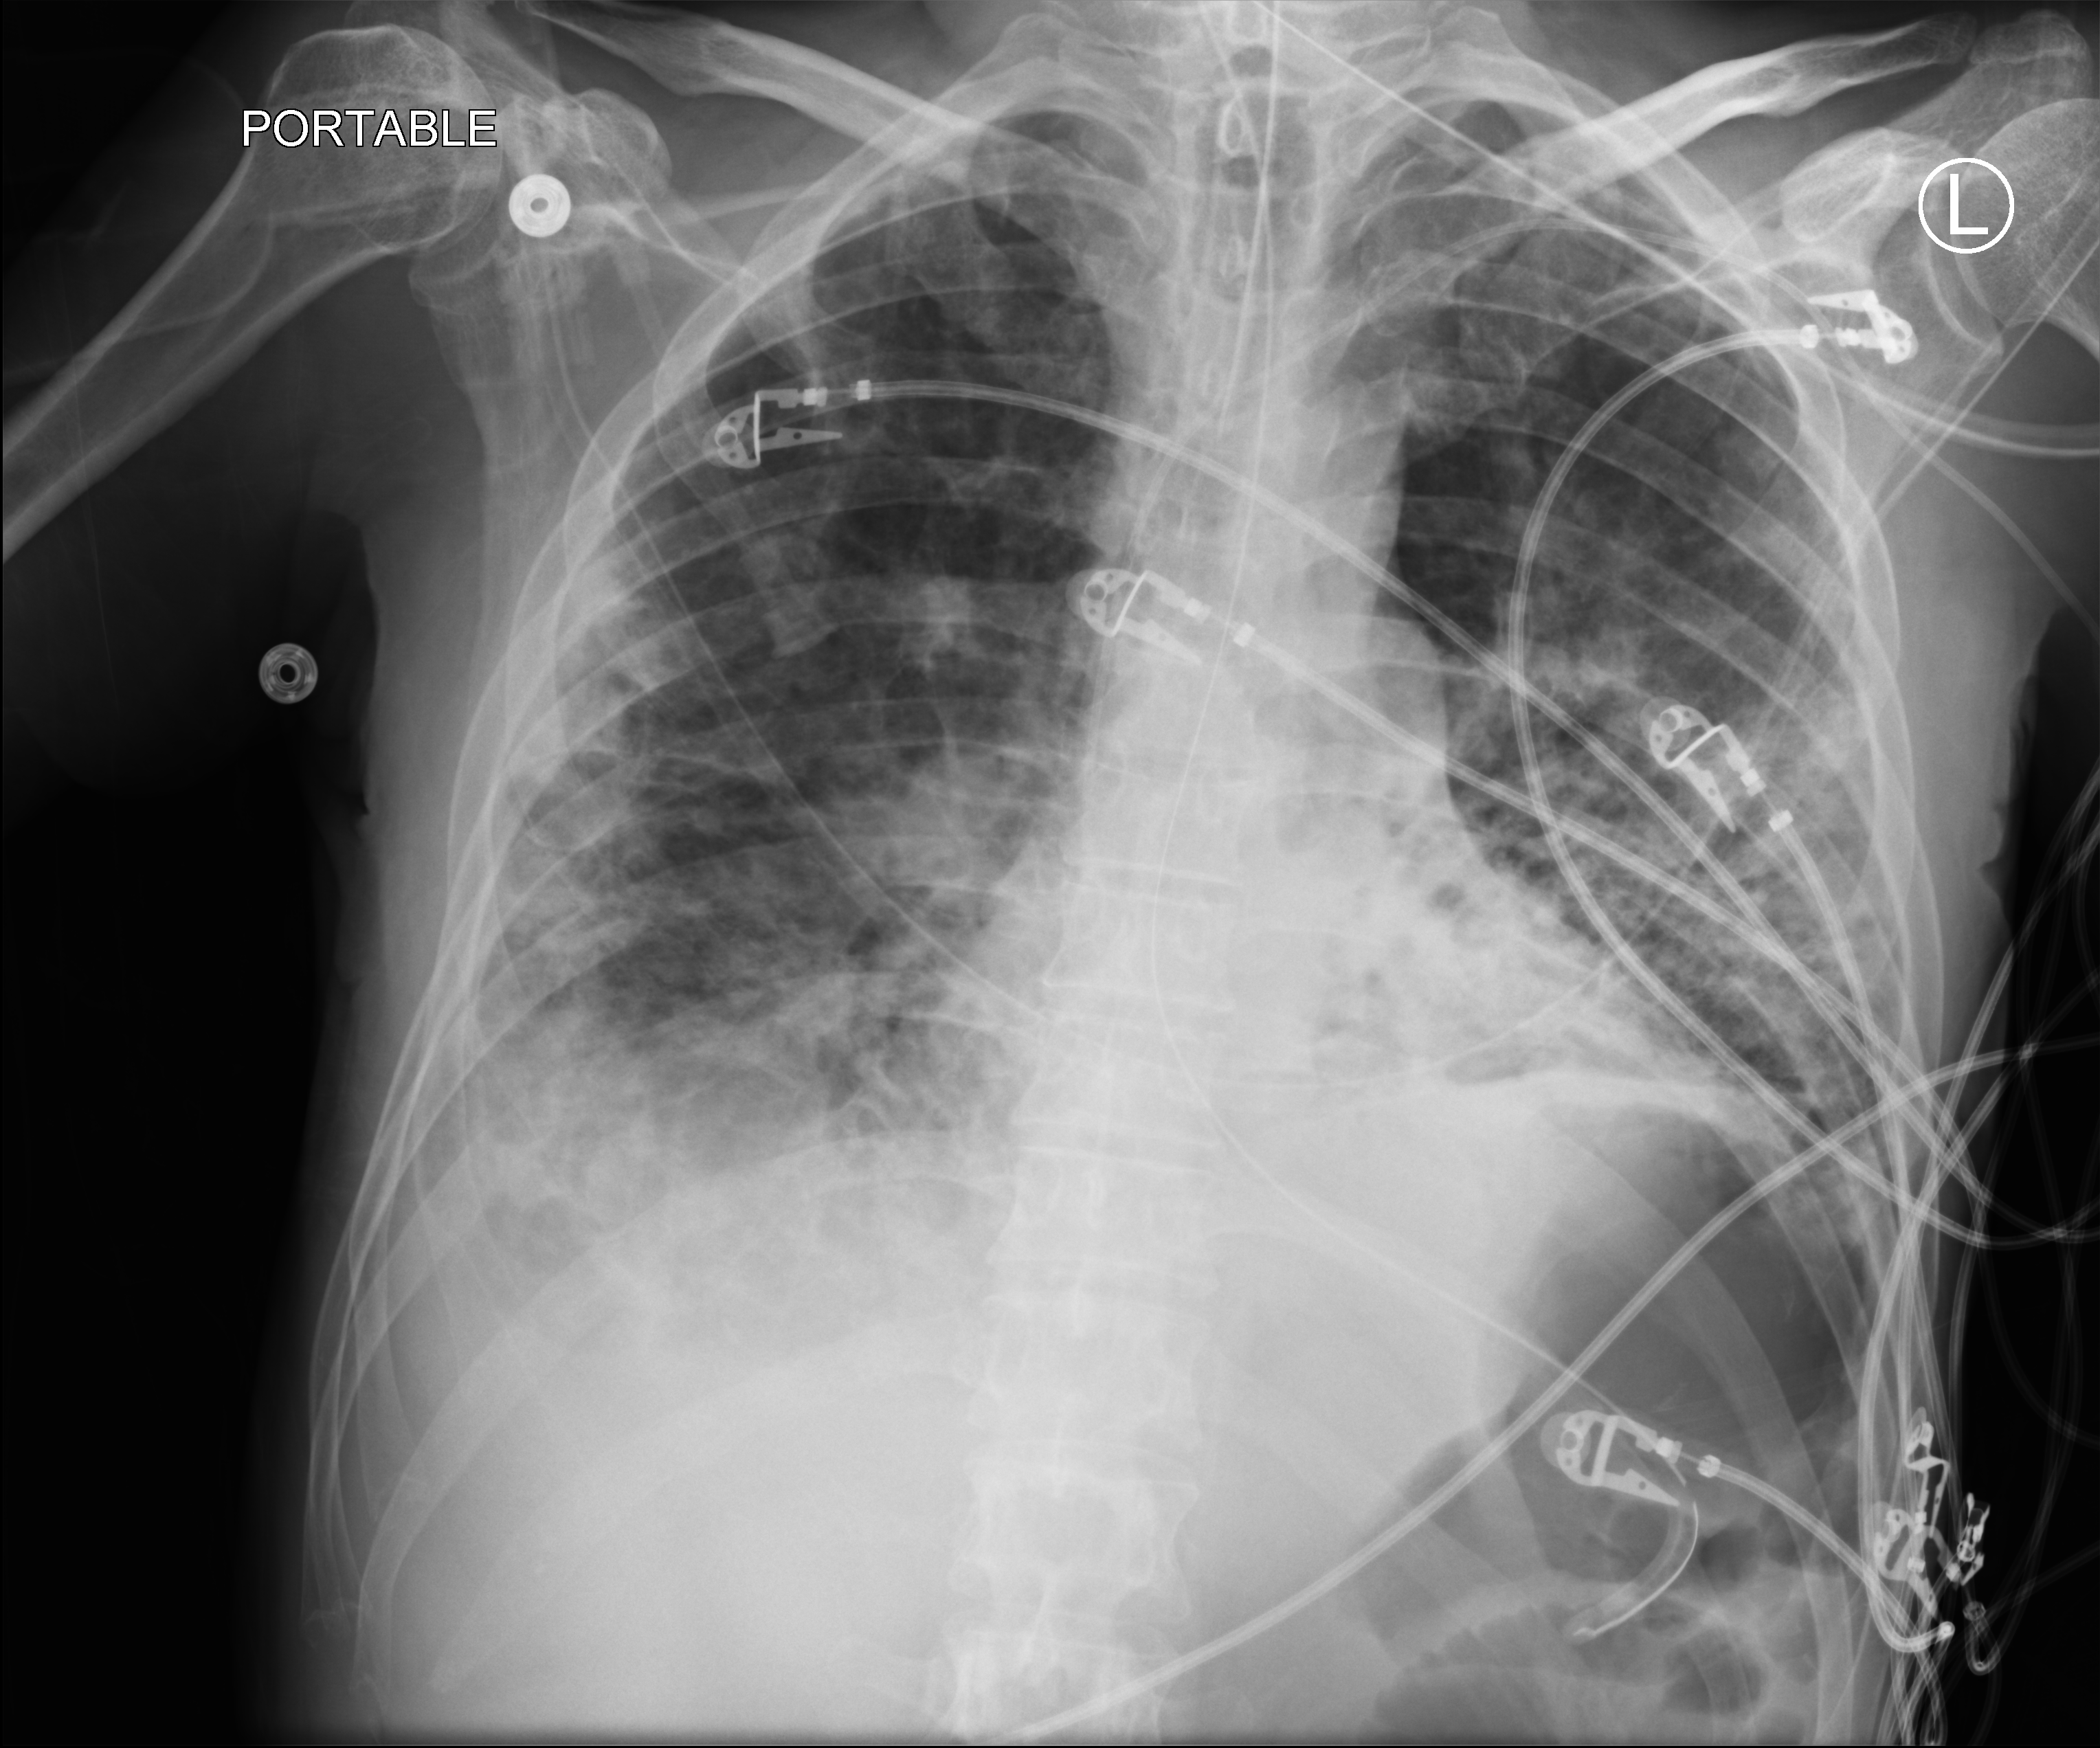
Bedside chest radiograph (computed radiography); anteroposterior (AP) projection. Patient hospitalised with COVID-19; male, aged 18–59 years.
Admission-level facts for this patient (not findings on this image; timing relative to this image not recorded): mechanically ventilated during this hospital stay: yes; COPD (admission record): no.